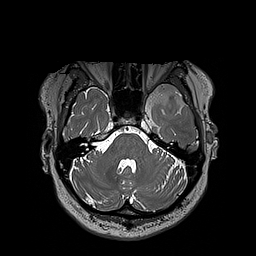
Brain MRI from a brain-tumour surgery series, one axial slice; slice 146 of 192 in the series (ordered by position); 1 mm slice thickness; 256 × 256 image matrix. From the clinical record (not read from this slice): histopathology: Oligodendroglioma; WHO grade: 3.
Structures marked on this image (expert manual segmentation):
- tumour: box from (x=124, y=83) to (x=197, y=112) px